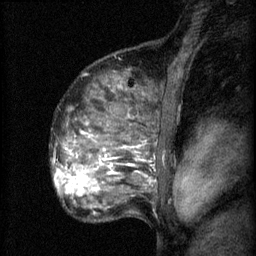
Breast MRI (dynamic contrast-enhanced), one sagittal slice. Position 46 of 60 along the scan axis. 3 images stored at this slice position (order not interpretable as contrast timing). 1.5 T. TE 4.2 ms, TR 8.2 ms. 256 × 256 image matrix, field of view 180 × 180 mm. Patient: female, 48 years.
Structures marked on this image (semi-automatic segmentation, software-assisted and operator-edited):
- analysis volume of interest (the breast-tissue region the enhancement analysis was run in; not a lesion): box from (x=61, y=138) to (x=153, y=201) px
- tumour enhancement mask (voxels above the 70 % enhancement threshold inside the analysis volume of interest): (x=61, y=164)–(x=100, y=197)